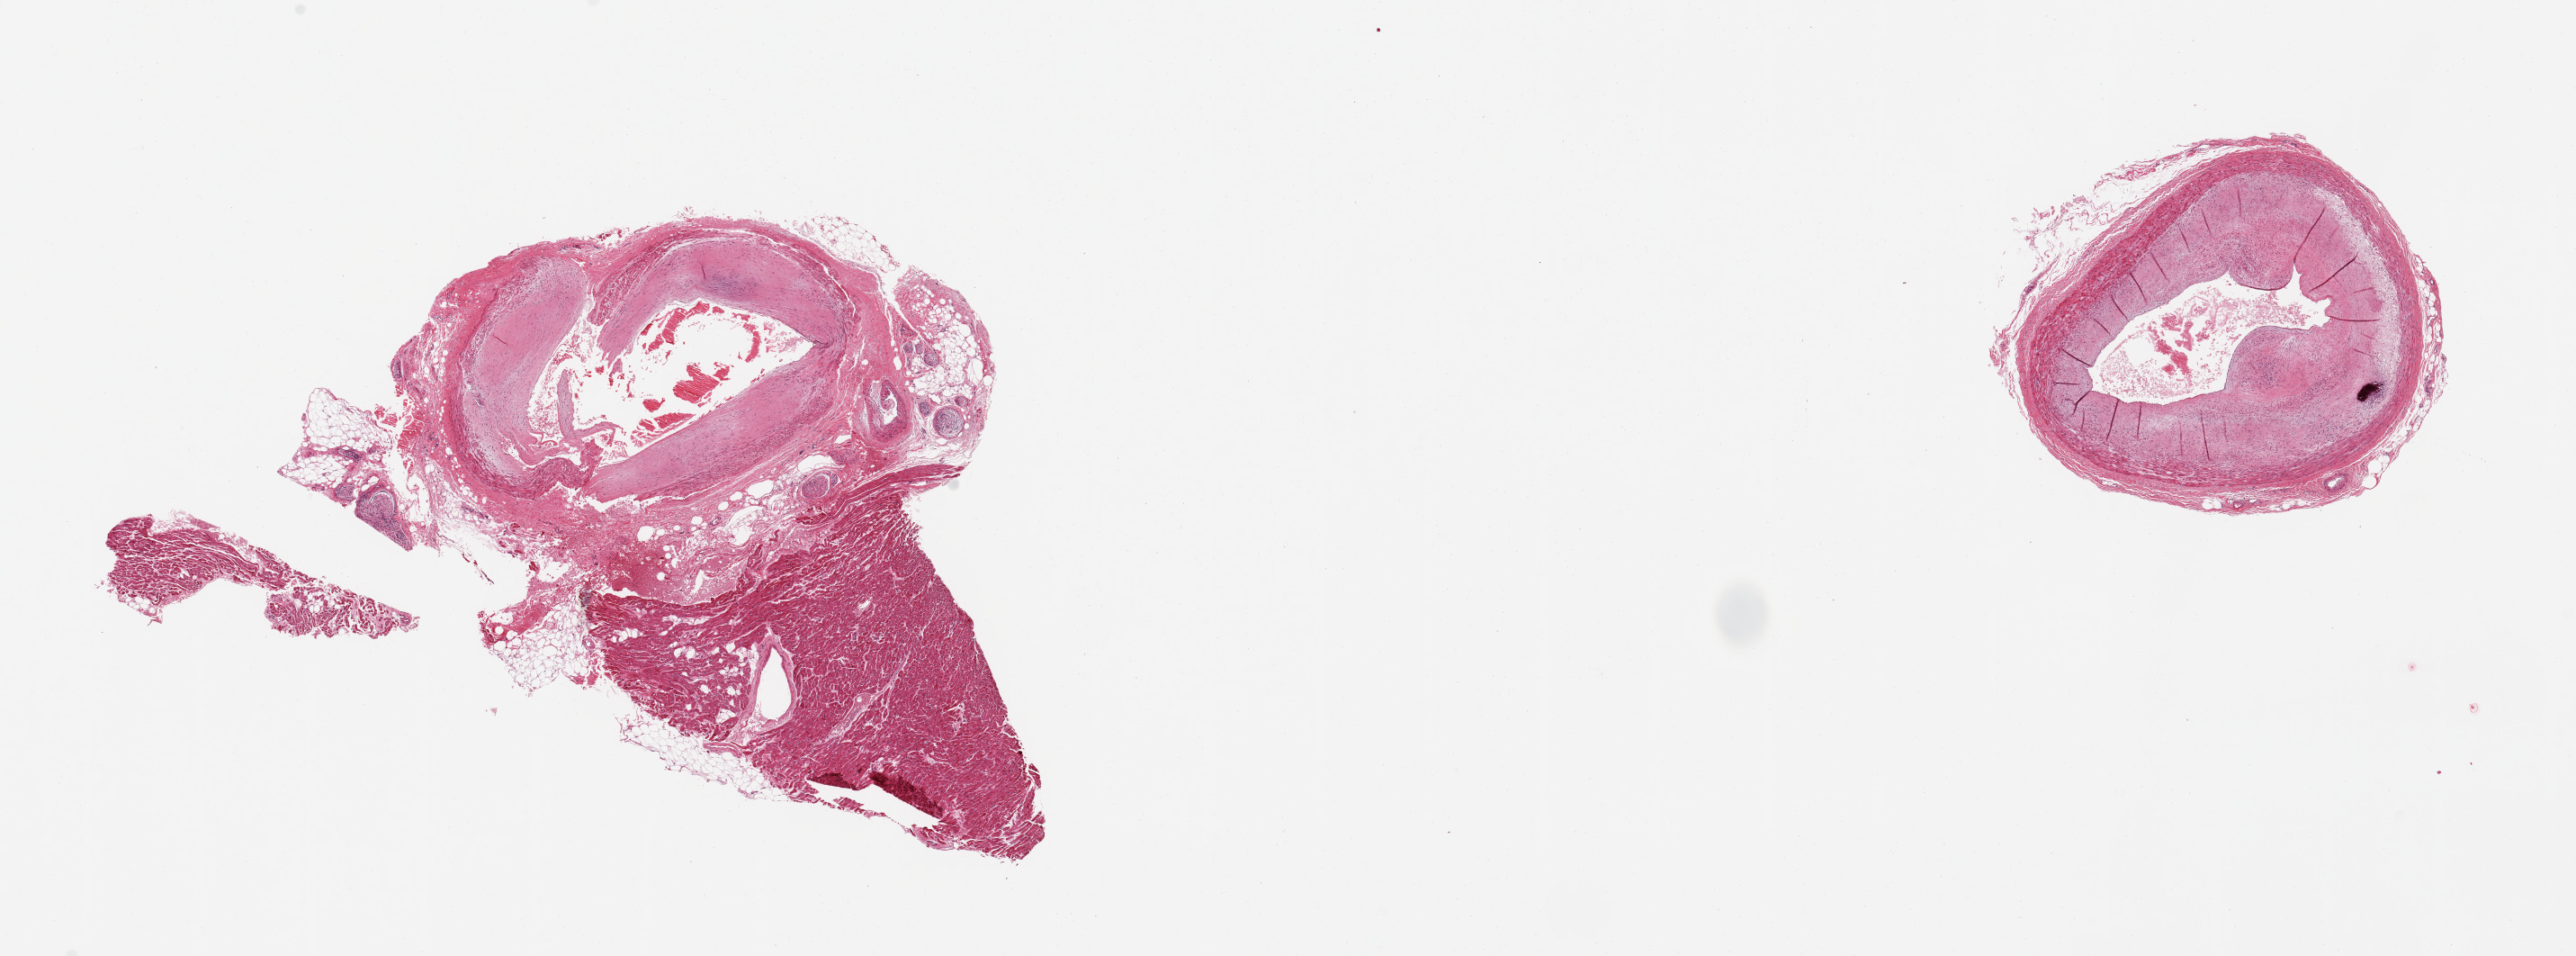
Whole-slide image, haematoxylin and eosin stain, whole scanned area (about 22.6 x 8.4 mm) shown as a low-resolution overview, PAXgene-fixed paraffin-embedded (PFPE) section, section of coronary artery (target tissue), tissue donor sample. Donor: female.
Review note (as recorded): 2 pieces; prominent sclerotic, partly calcified plaque; 1 piece has 50% adjacent myocardium and fibrofatty tissue.